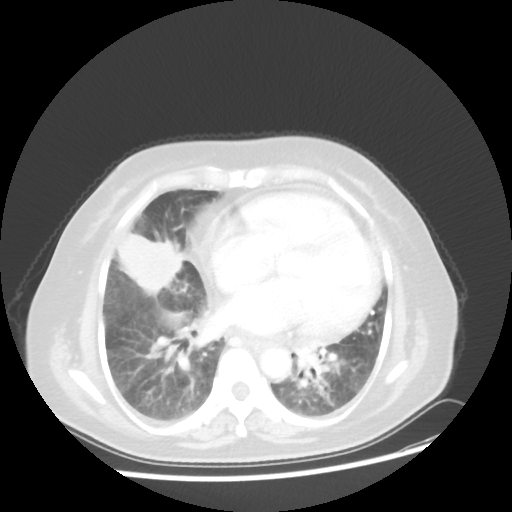
Chest CT, one axial slice; position 19 of 45 along the scan axis; 100 kVp; lung window (W 1500 / L -600 HU); 5 mm slice thickness; 512 × 512 image matrix. Patient: female, 67 years. From the clinical record (not read from this slice): clinical TNM (as recorded): T2a N3 M1a.
Structures marked on this image (rectangle marked by the reading radiologist):
- lung tumour (recorded histology: adenocarcinoma): bounding box (x1, y1, x2, y2) in pixels: (116, 227, 190, 298)